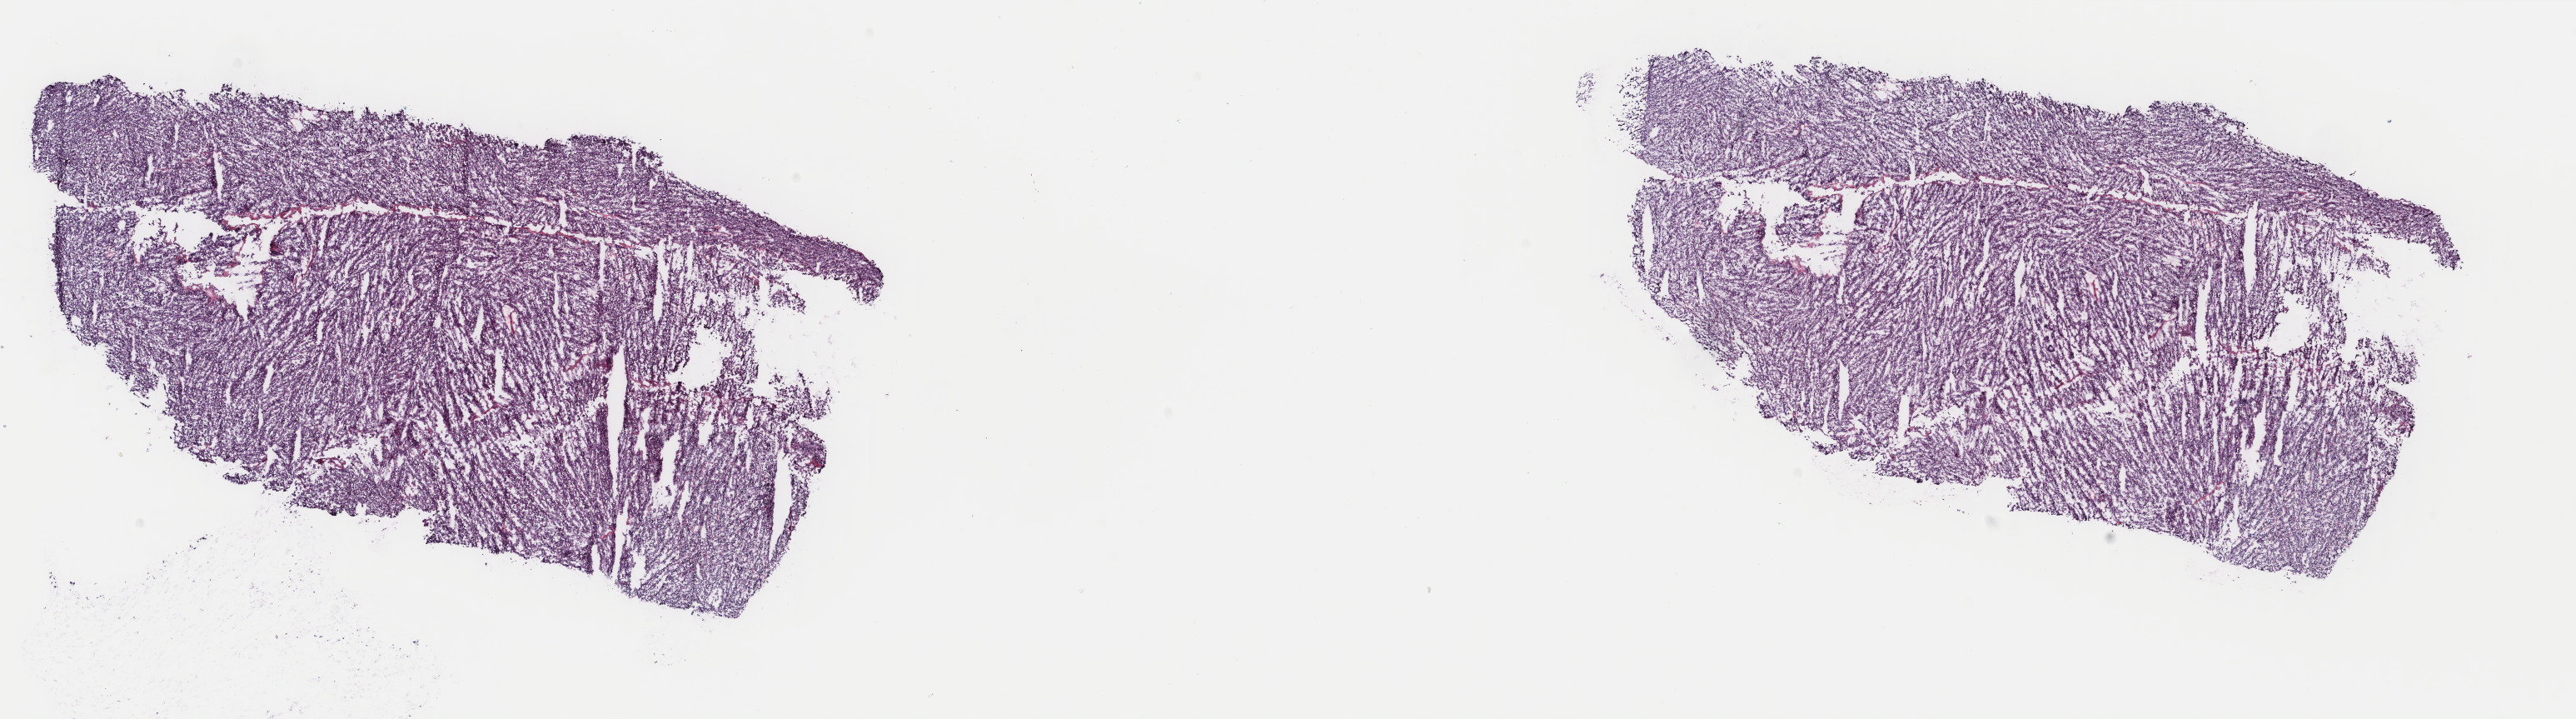
Digitized H&E tissue section (whole slide) — shown as a low-resolution overview of the whole scanned area (about 24.6 x 6.9 mm, acquisition: 40x scan). Frozen section. Sample: primary tumour, adrenal gland. Patient: male, age at initial diagnosis 55 years. Pathologist review of this section (percent, as recorded): tumour cells 100%, tumour nuclei 95%.
Pathologic diagnosis: Pheochromocytoma, malignant.